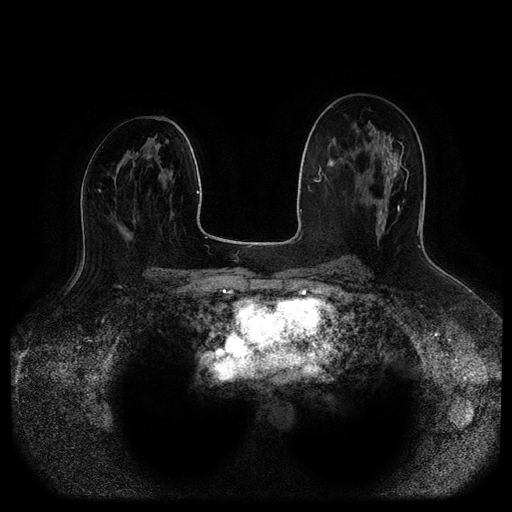
Breast MRI (dynamic contrast-enhanced, multi-phase), one axial slice. Position 52 of 116 along the scan axis. Dynamic contrast-enhanced series, time point 2 of 5 at this slice position (early post-contrast). 1.5 T. TE 2.6 ms, TR 5.2 ms. 2 mm slice thickness. 512 × 512 image matrix, field of view 380 × 380 mm. Female patient, age 45 years.
Outlined on this slice (semi-automatically segmented with operator editing):
- breast lesion (labelled benign in the annotation): bounding box <373,156,398,224> (left, top, right, bottom; pixels)